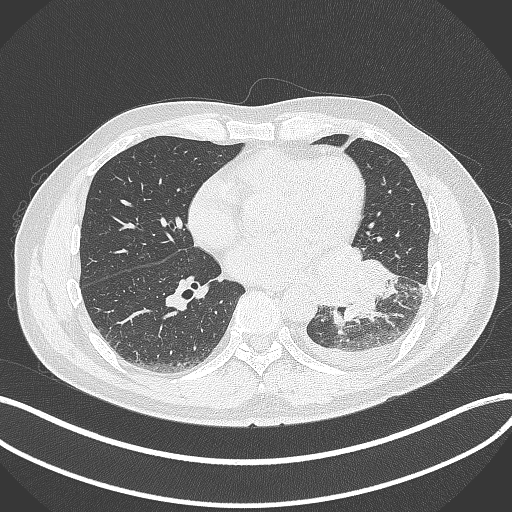
Chest CT, one axial slice; slice 152 of 342 in the series (ordered by position); 120 kVp; lung window (W 1500 / L -600 HU); 512 × 512 image matrix. Male patient, age 58 years. Case-level facts recorded for this patient, not image findings: clinical TNM (as recorded): T3 N1 M1b; histopathological grade: G3.
Outlined on this slice (rectangle marked by the reading radiologist):
- lung tumour (recorded histology: small cell carcinoma): bounding box [x1, y1, x2, y2] px = [314, 239, 399, 321]